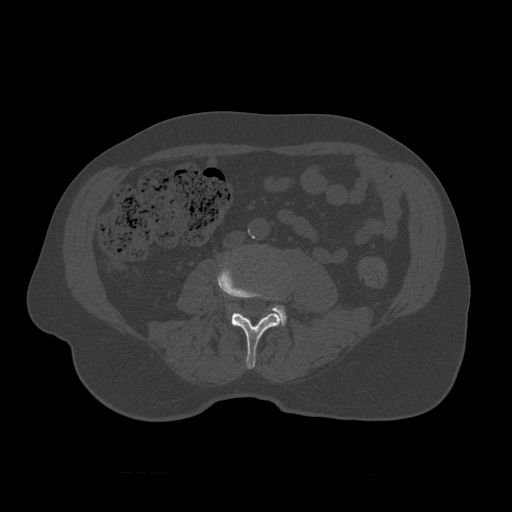
CT including the spine, one axial slice; slice 293 of 450 in the series (ordered by position); reconstruction kernel STANDARD; 120 kVp; bone window (W 1800 / L 400 HU); 1.25 mm slice thickness; 512 × 512 image matrix, field of view 405 × 405 mm. Patient age 75 years. Case-level facts recorded for this patient, not image findings: primary cancer: prostate.
Outlined on this slice (semi-automatic segmentation, software-assisted and operator-edited):
- L3 vertebra: box from (x=217, y=265) to (x=282, y=370) px
- L4 vertebra: (x=229, y=294)–(x=287, y=327)